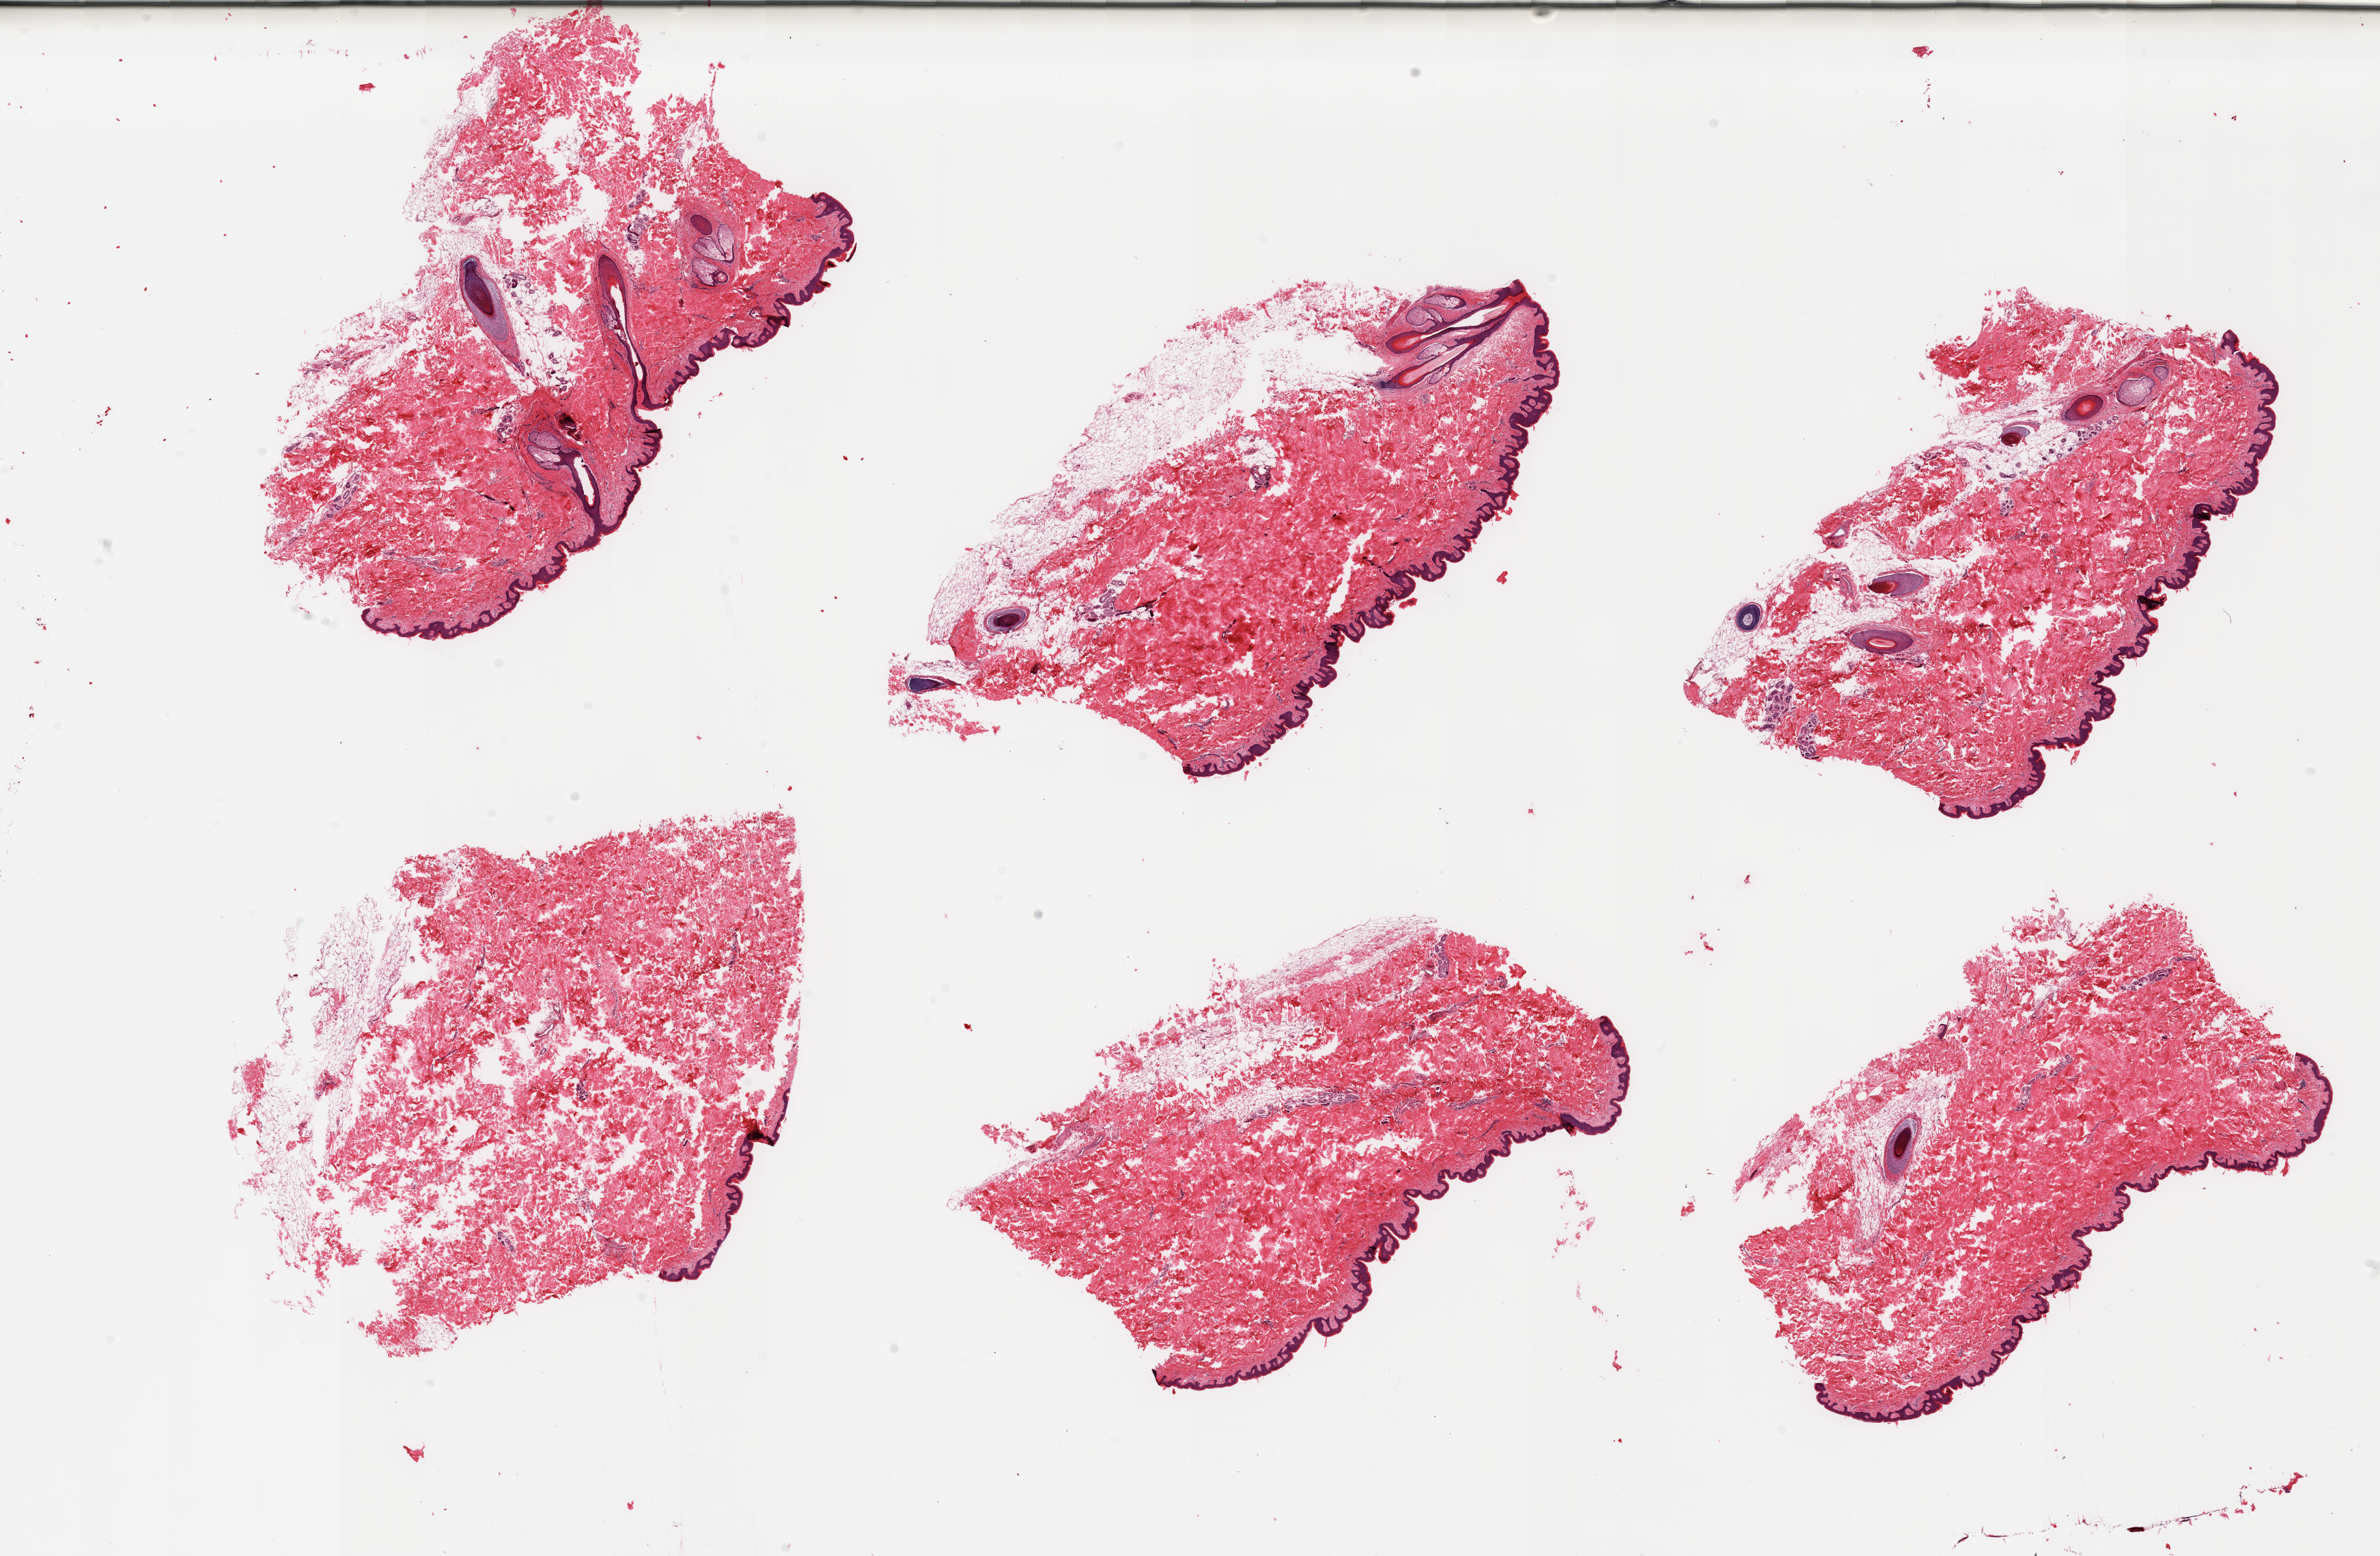
Whole-slide image, haematoxylin and eosin stain, brightfield — shown as a low-resolution overview of the whole scanned area (about 27.6 x 18.0 mm); PAXgene-fixed paraffin-embedded (PFPE) section; sampled site (target tissue): skin of suprapubic region; tissue donor sample. Donor: male.
Reviewer comment on this tissue sample: 6 pieces, minimal dermal fat, squamous epithelium, ~60 microns.